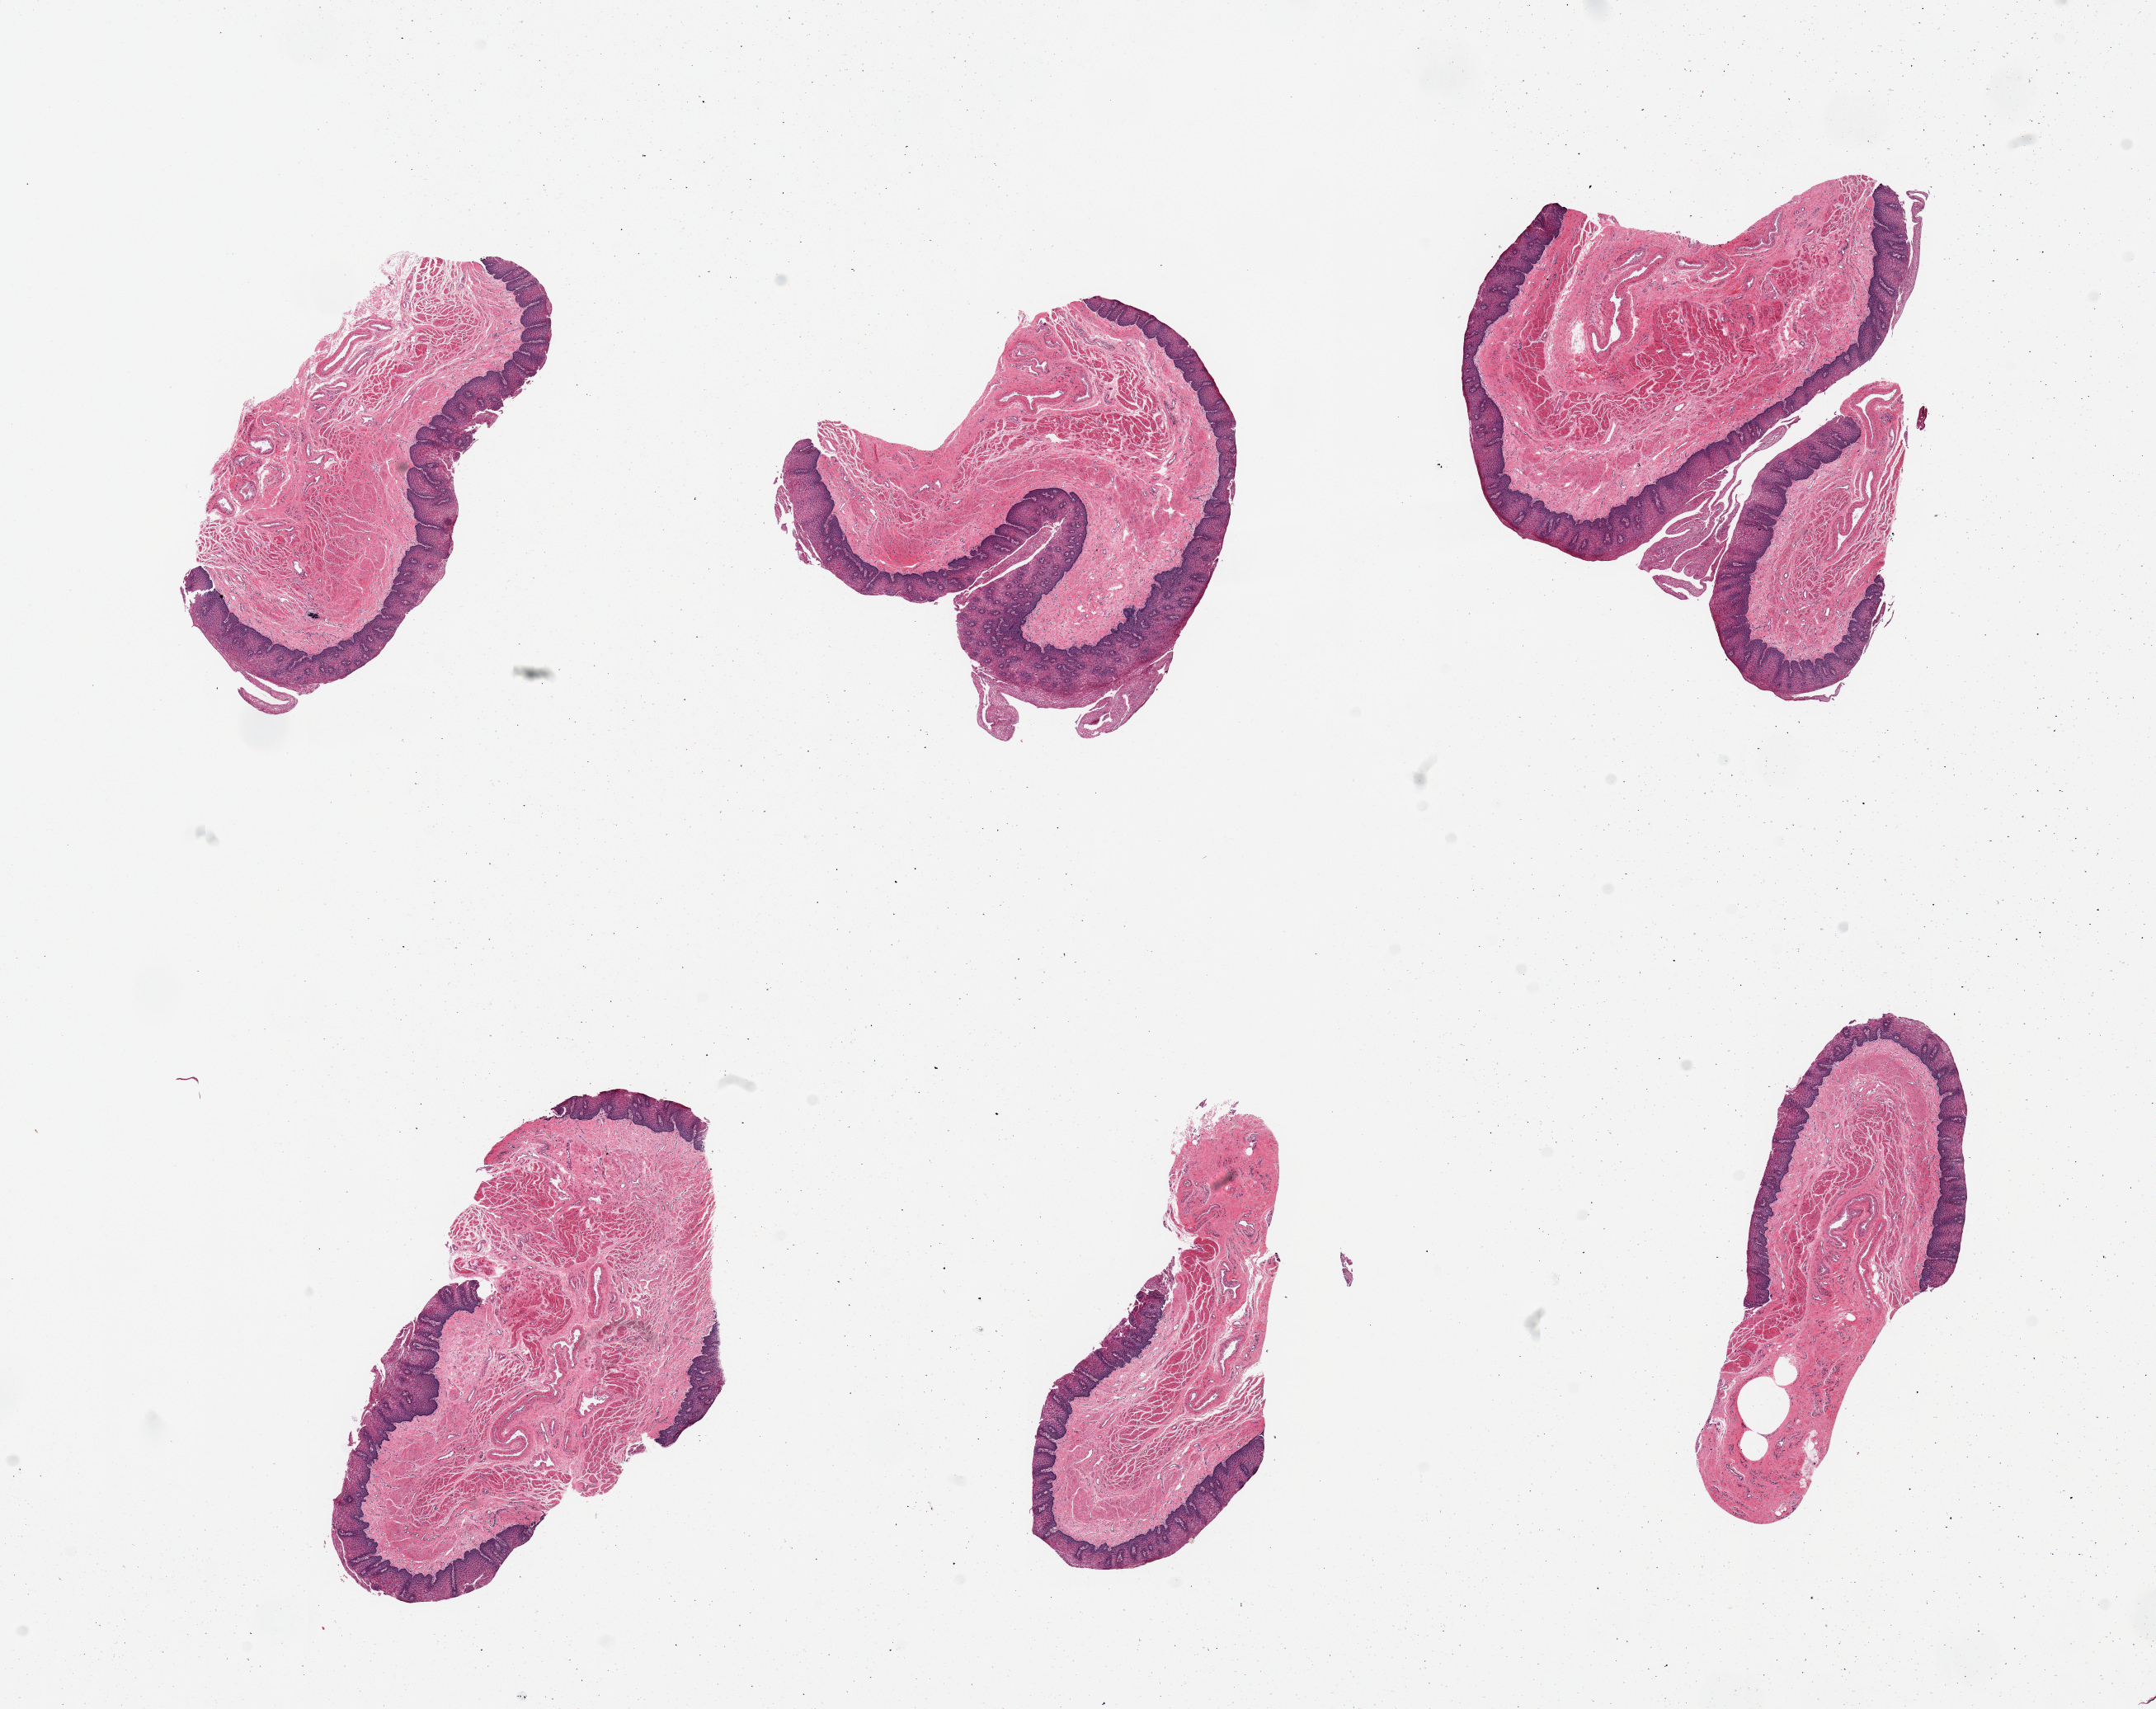
Digitized hematoxylin and eosin (H&E)-stained section, whole scanned area (about 20.7 x 16.4 mm) shown as a low-resolution overview; PAXgene-fixed, paraffin-embedded tissue; sampled site (target tissue): esophageal mucous membrane; donor tissue sample. Male donor.
Pathologist's review note for this sample: 6 pieces.